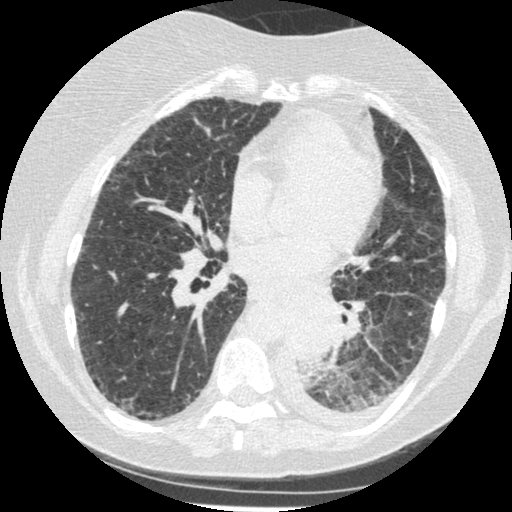
Chest CT (low-dose screening protocol), one axial image, third screening round (two years after baseline), lung window (W 1500 / L -600 HU), slice 238 of 341 in the series, 512 × 512 image matrix, field of view 310 × 310 mm. Female, age 60 years at enrolment.
Expert-annotated lung lesion, bounding box <276,303,343,375> (left, top, right, bottom; pixels). Screening reader's record for this exam (one nodule recorded; not confirmed to be the boxed lesion): non-calcified nodule or mass ≥4 mm, left lower lobe, 54 × 38 mm, smooth margins, soft tissue attenuation, pre-existing on the prior screen: yes; interval growth: yes.